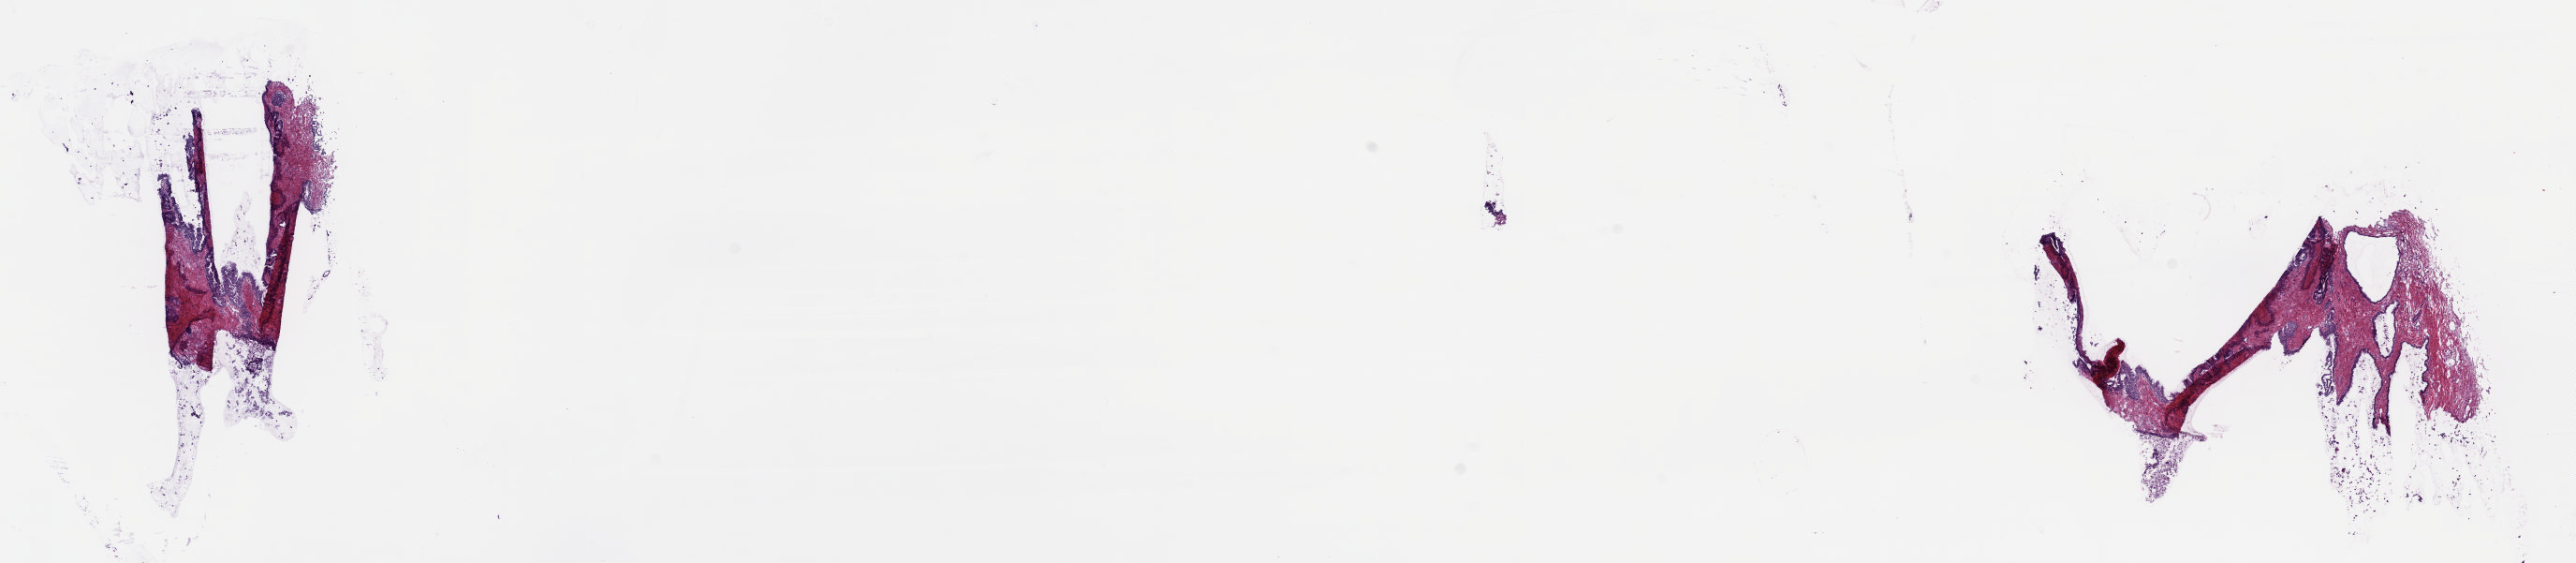
H&E-stained whole-slide image — low-resolution overview of the scanned area, about 21.8 x 4.8 mm (from a 20x scan). Frozen section from the top of the tissue portion. Bladder, solid tissue normal (non-tumour tissue) sample. Patient: male, age at initial diagnosis 69 years. Composition of this section per pathologist review: tumour cells 0%, tumour nuclei 0%, normal cells 100%, stromal cells 0%, necrosis 0%. Infiltration values recorded for this section: lymphocyte infiltration 2%, monocyte infiltration 0%, neutrophil infiltration 0%.
This section: solid tissue normal sample (biorepository sample class). Patient diagnosis: Transitional cell carcinoma.